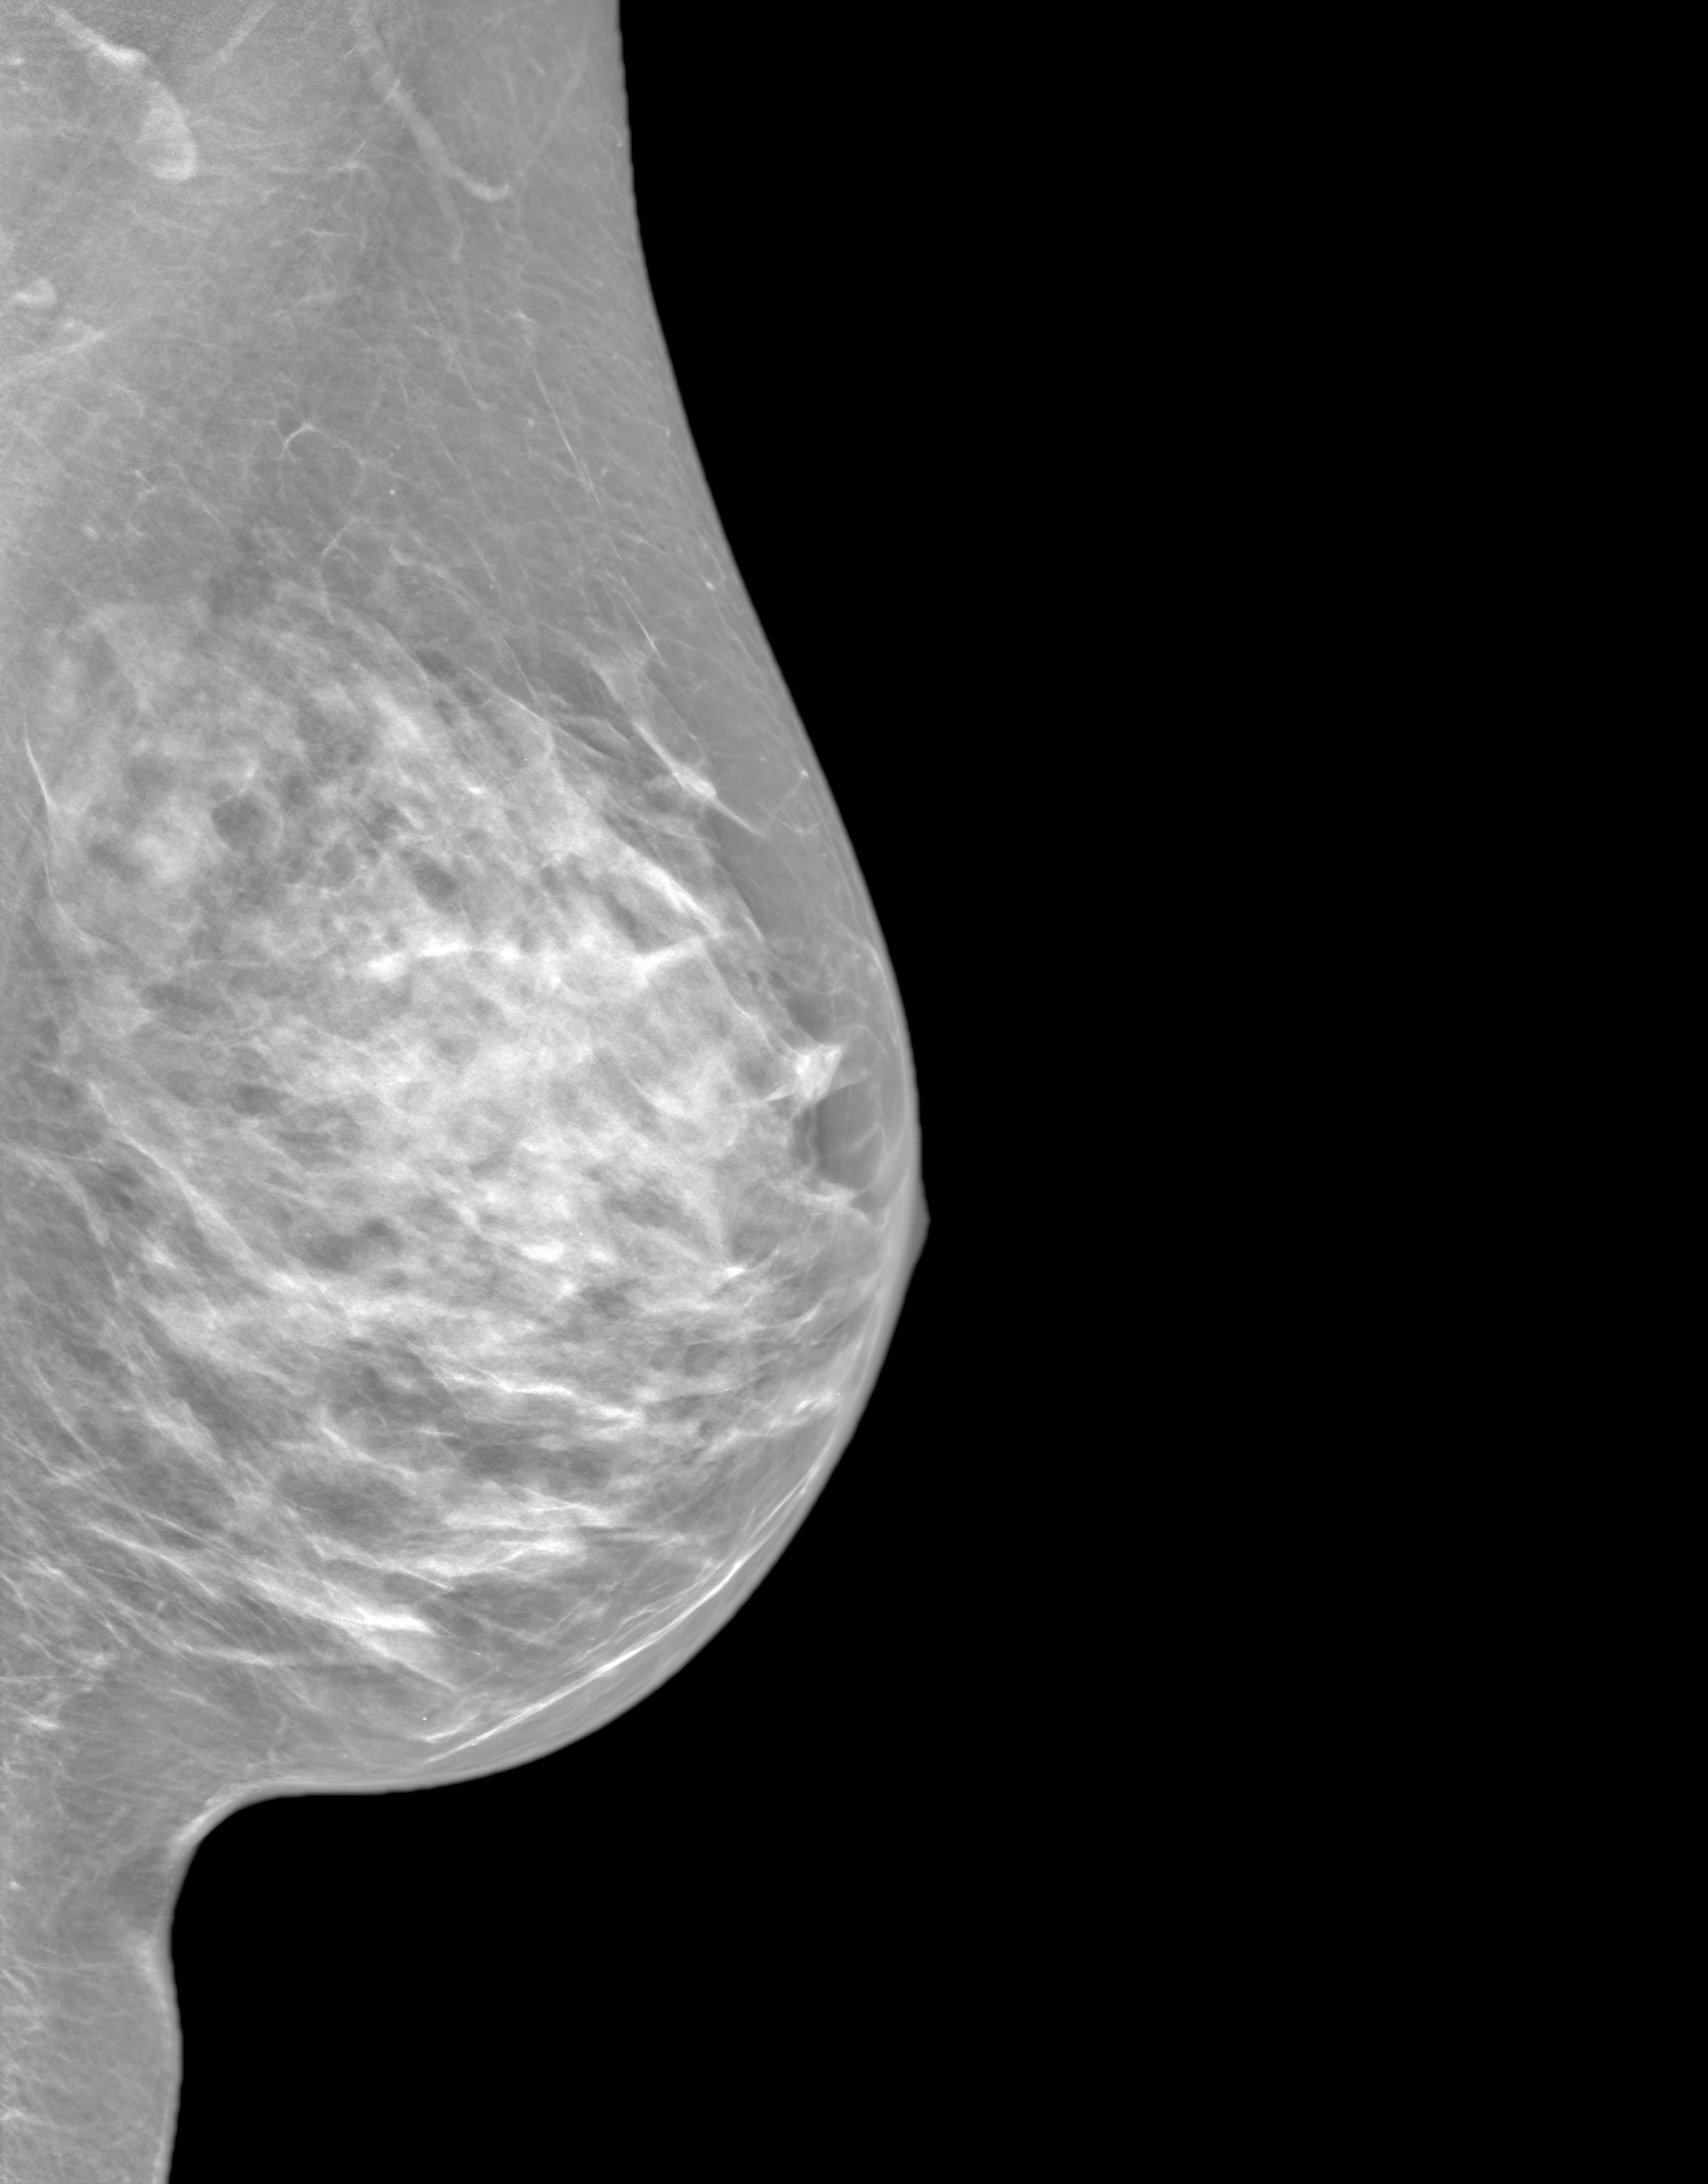
Synthetic 2-D view generated from a tomosynthesis acquisition (not an FFDM exposure); left breast; medio-lateral oblique projection; annual screening mammography examination. Patient: female, 64 years.
- breast density at the screening exam (both breasts): extremely dense (BI-RADS density category d)
- final BI-RADS category for the screening round (tomosynthesis exam, both breasts): category 2
- recall: no recall after this screen